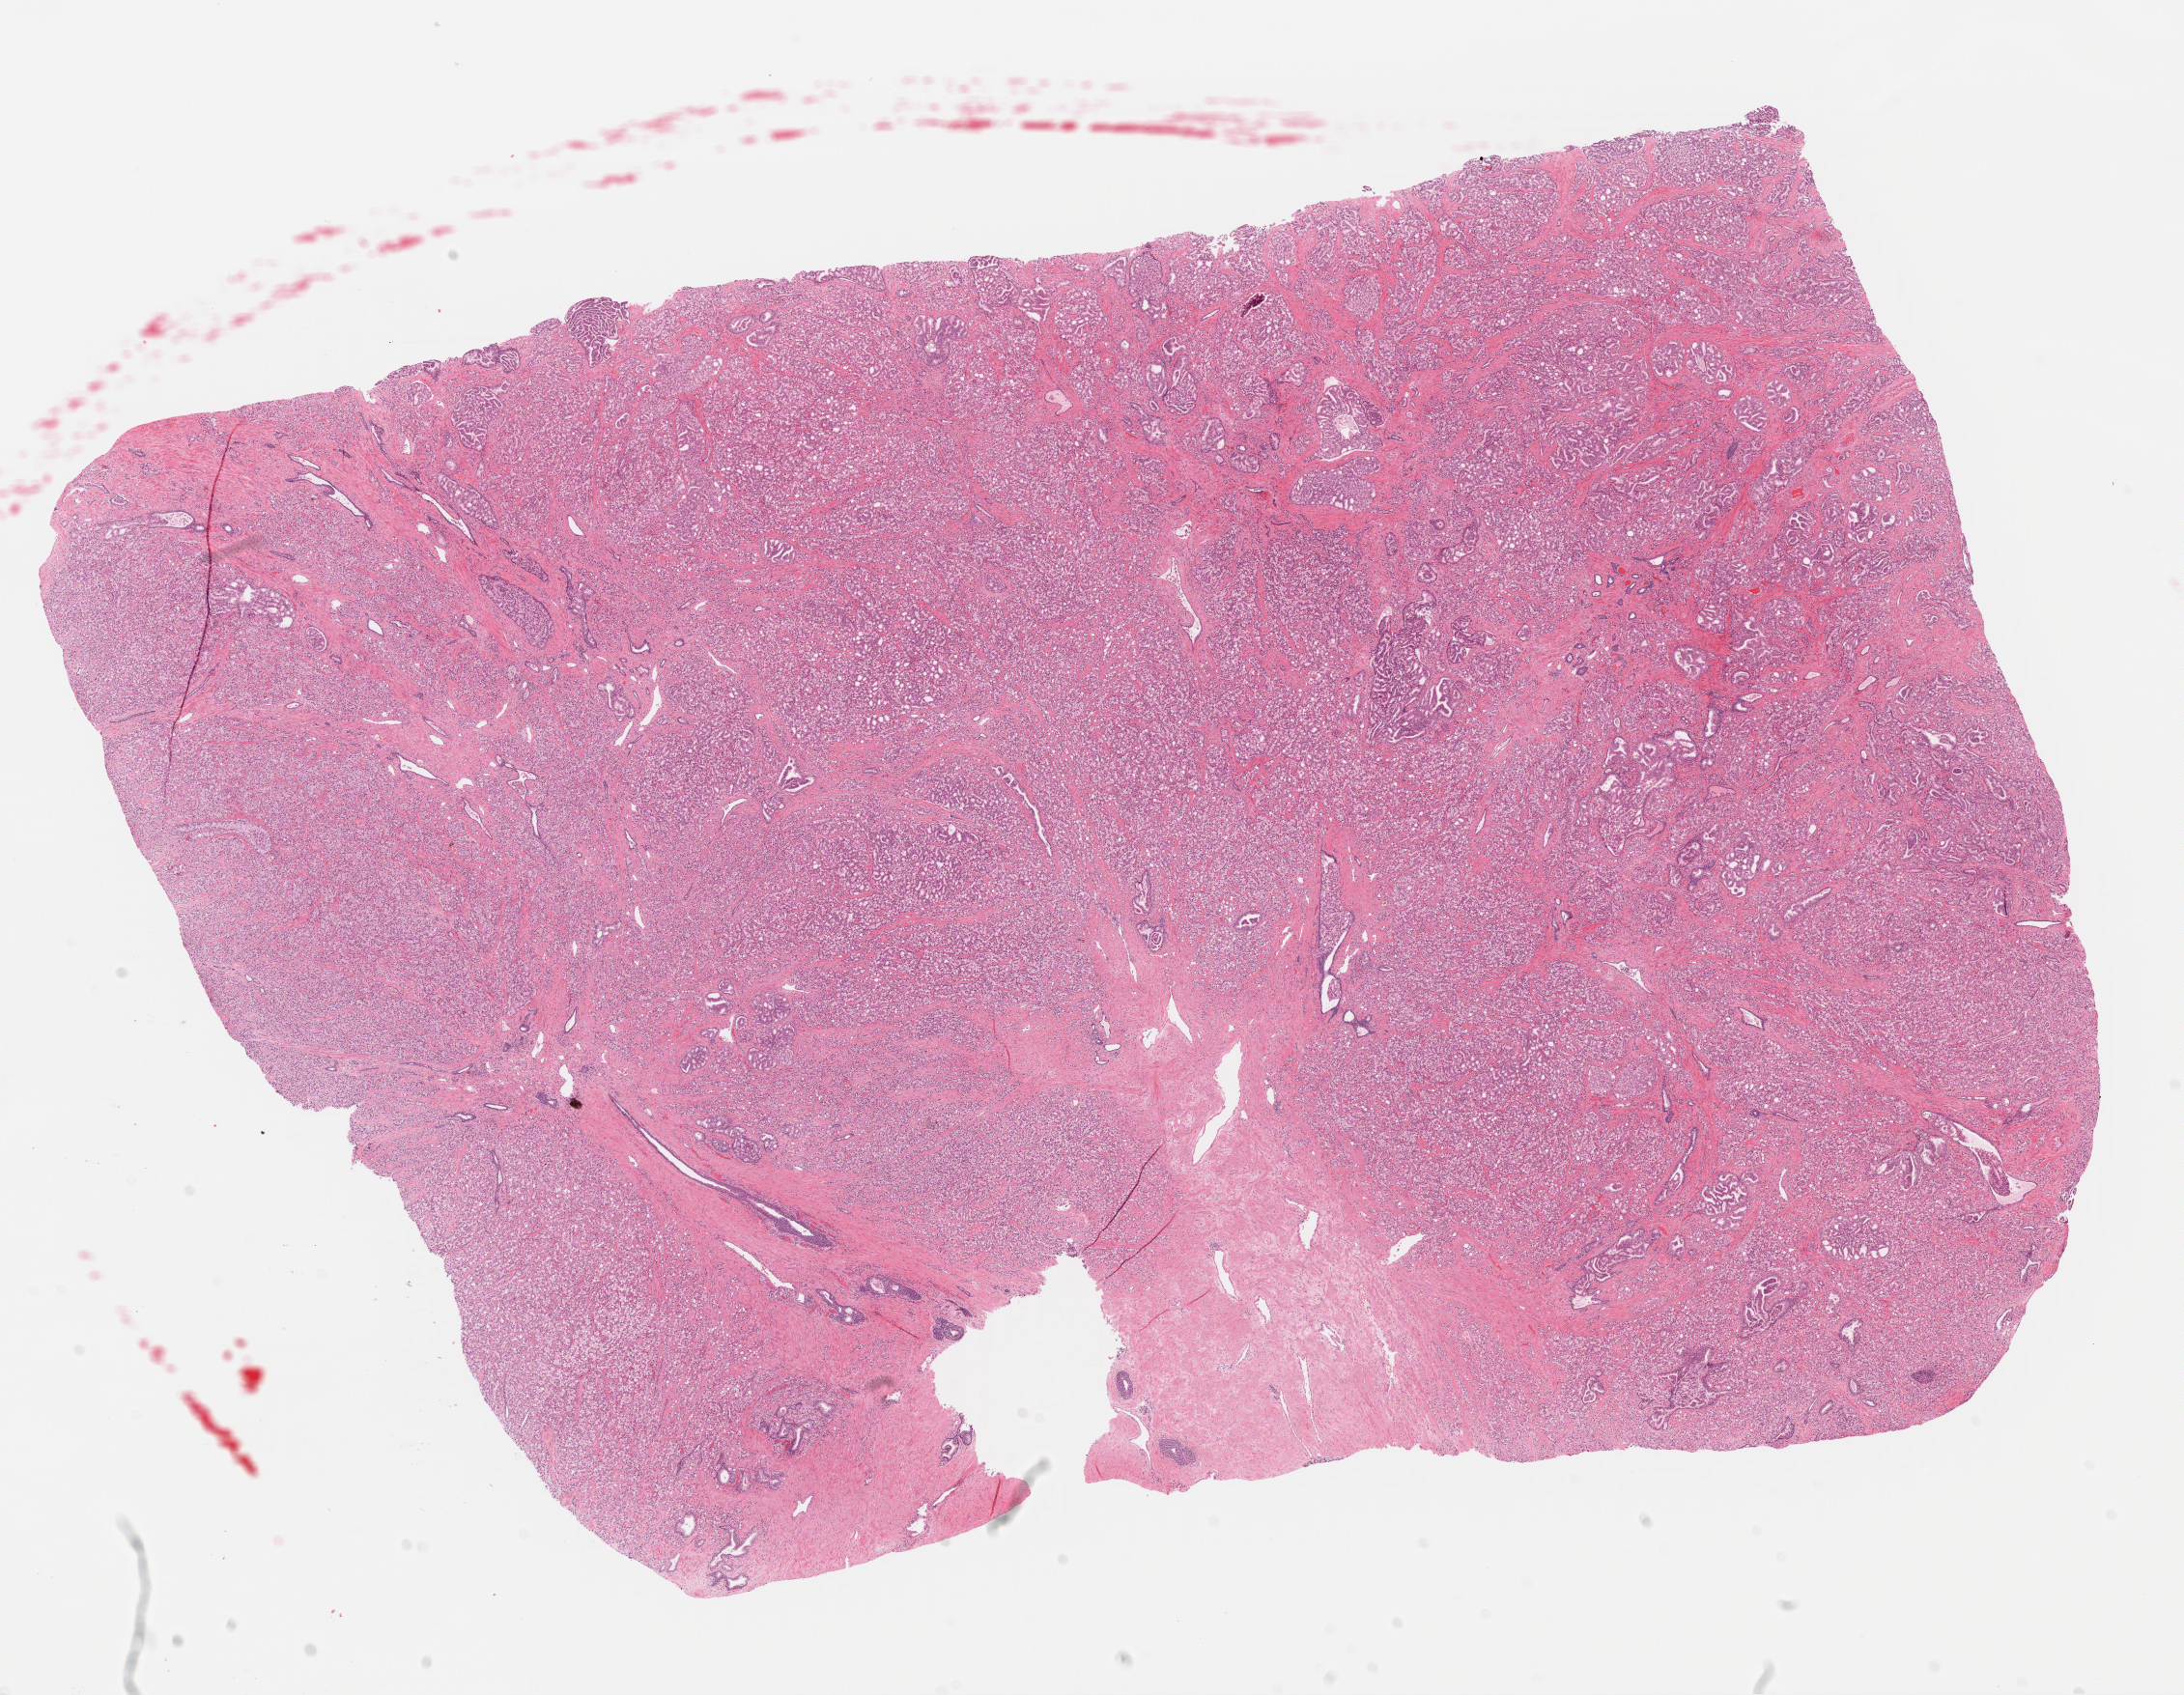
Digitized H&E tissue section (whole slide), a low-resolution overview of the entire scanned area, about 17.8 x 13.8 mm, formalin-fixed paraffin-embedded (FFPE) diagnostic section, sample: primary tumour, prostate. Male patient; age at initial diagnosis 53 years. Gleason score: 9 (4+5).
• laterality: bilateral
• histologic diagnosis: Adenocarcinoma, NOS (prostate gland)
• lymph nodes positive (case pathology): 0 of 9 examined